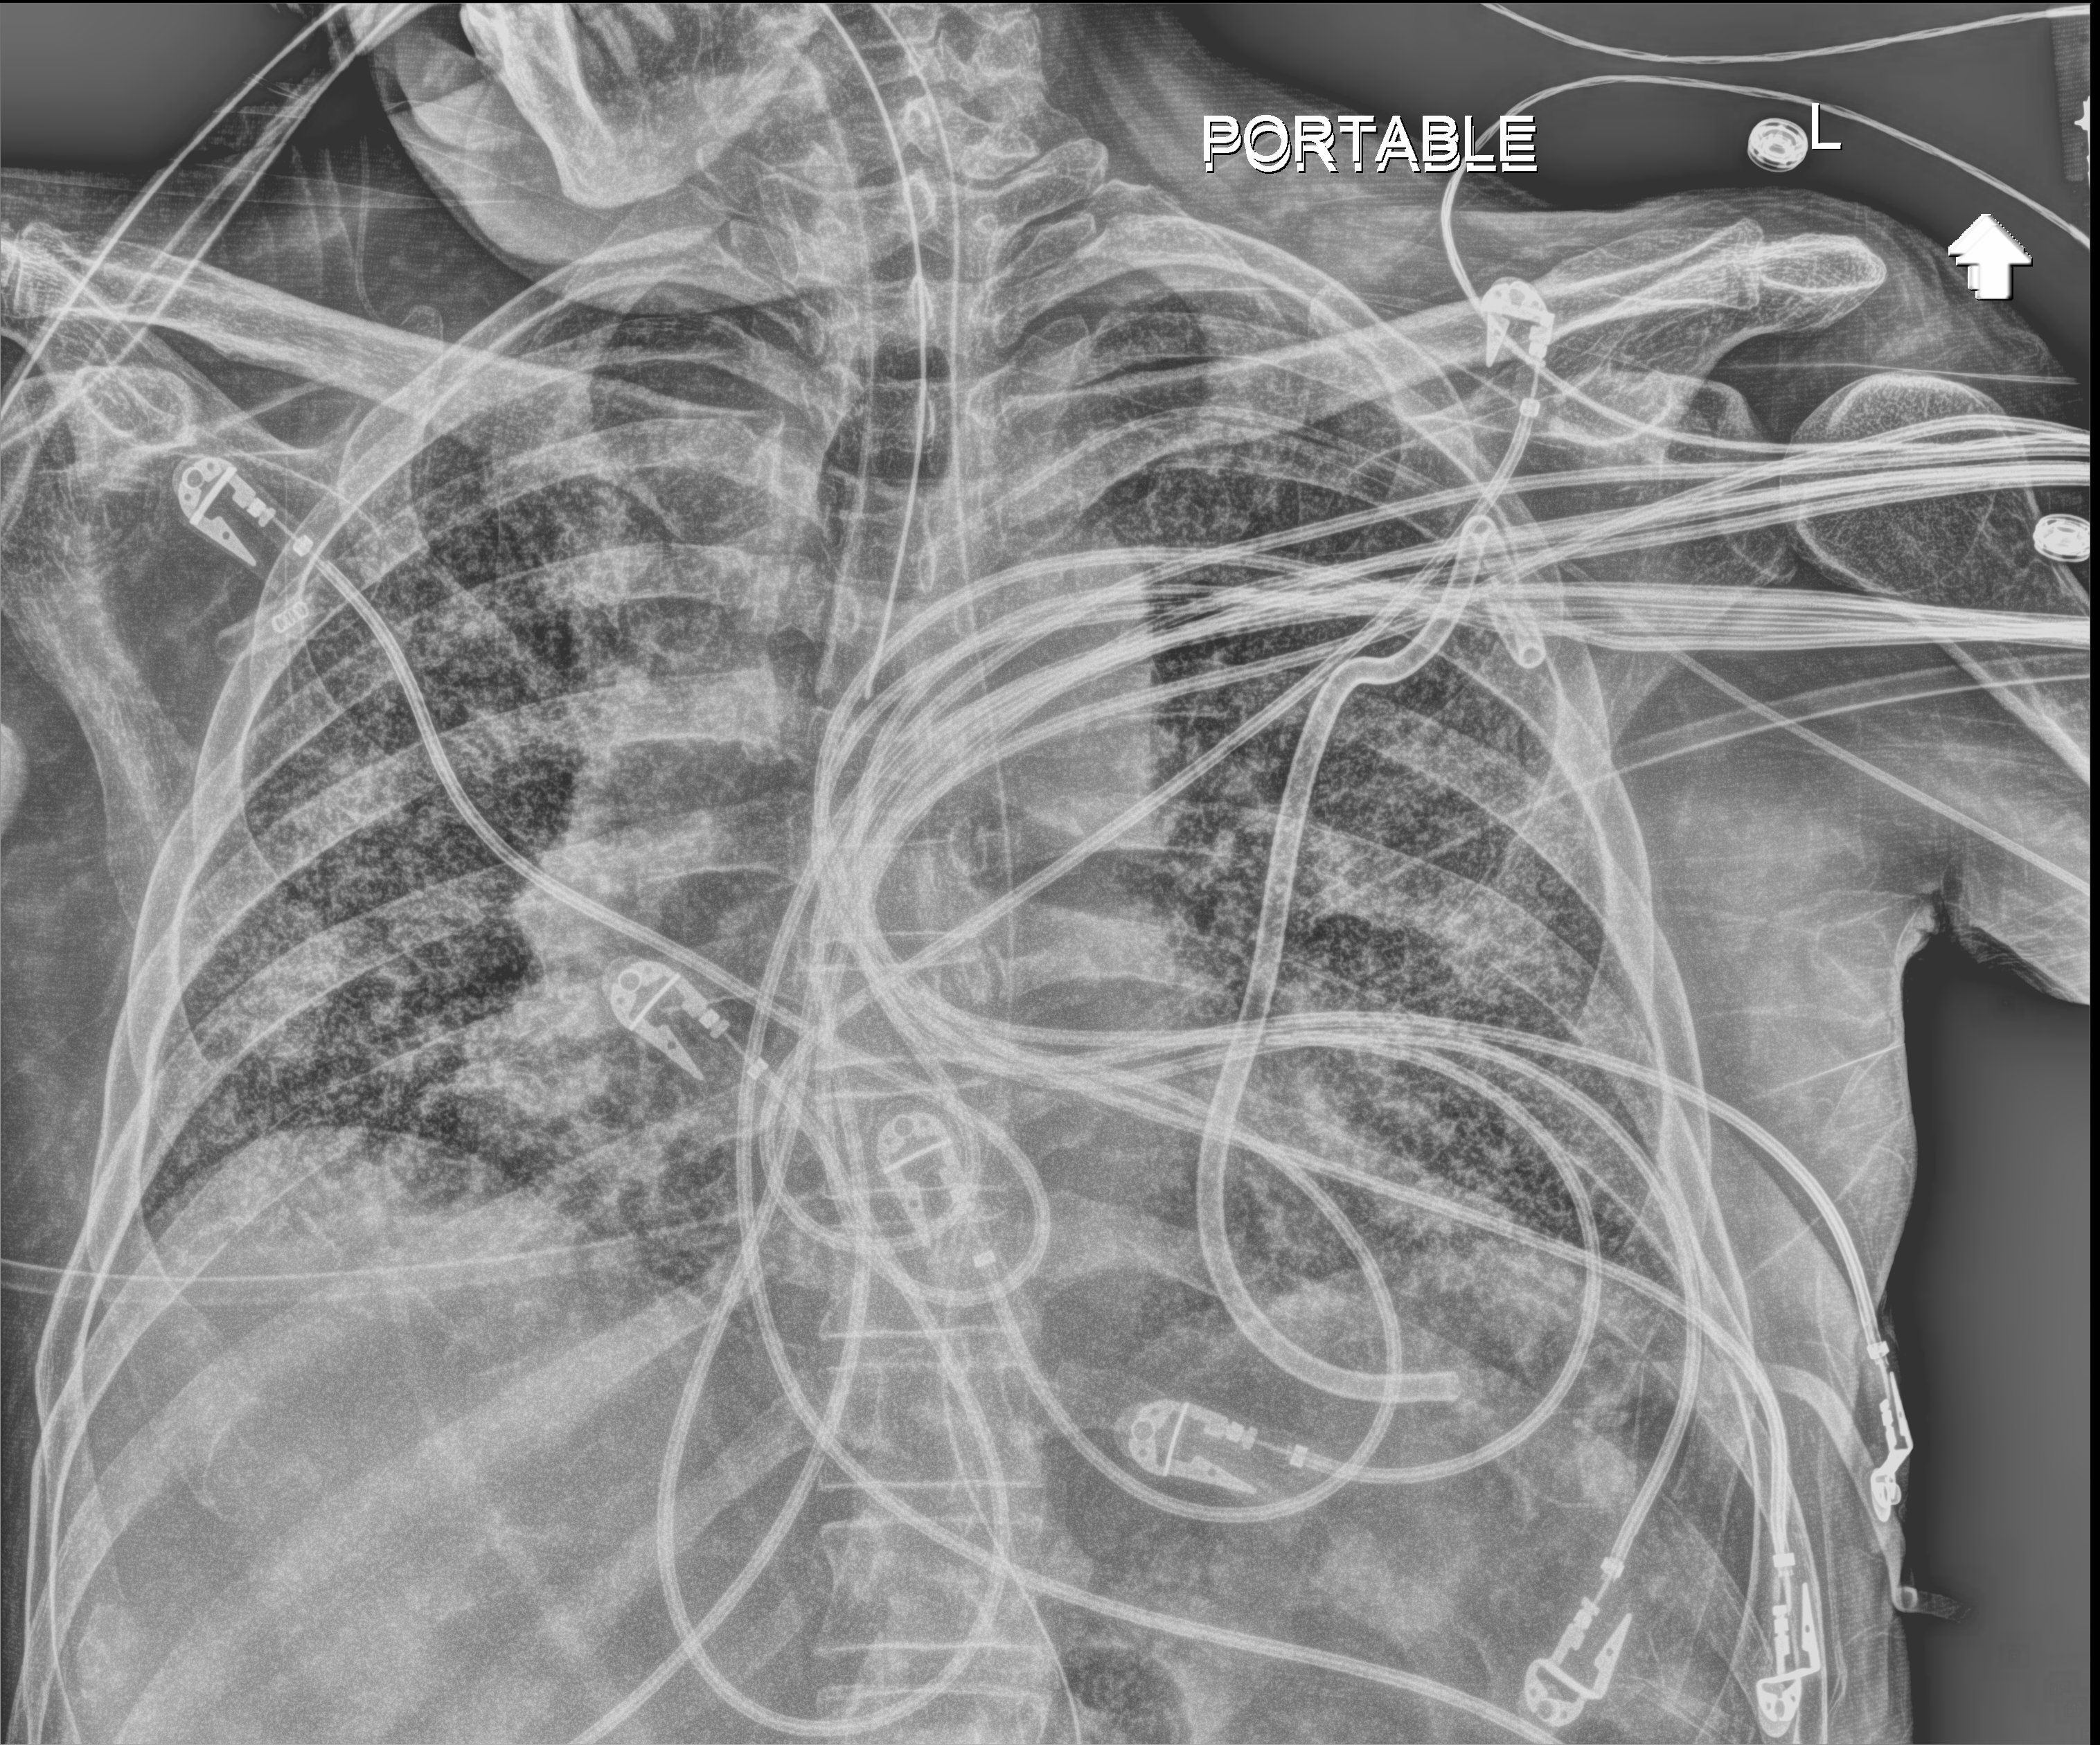
Chest radiograph, anteroposterior (AP) projection. Male patient hospitalised with COVID-19, age 60–74 years.
Admission-level facts for this patient (not findings on this image; timing relative to this image not recorded):
- mechanically ventilated during this hospital stay: yes
- admitted to intensive care during this hospital stay: yes